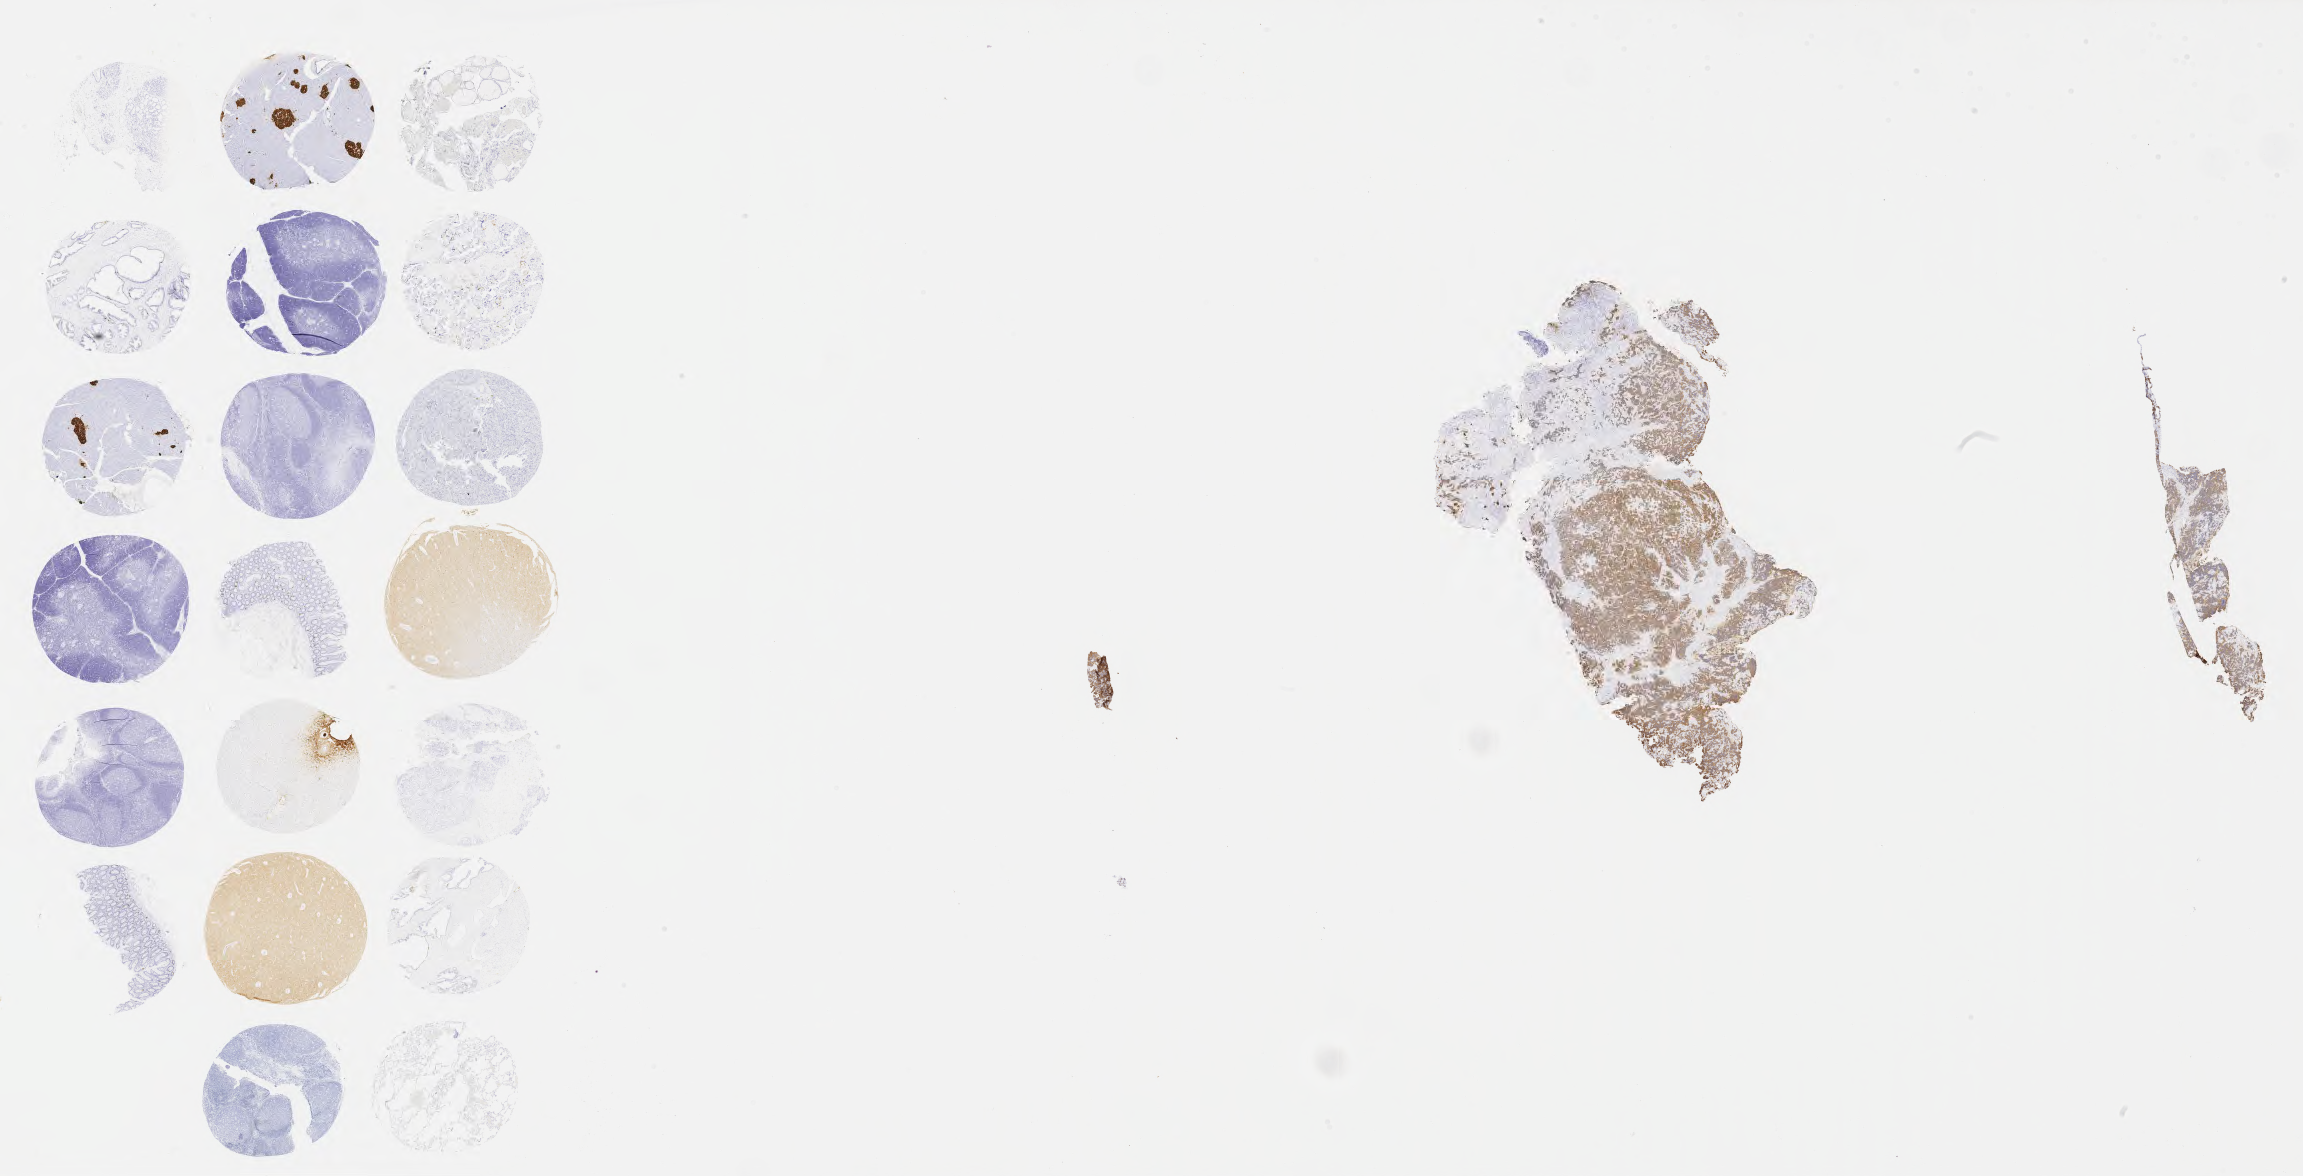
Whole-slide image, immunohistochemical stain for chromogranin, a low-resolution overview of the entire scanned area, about 37.2 x 19.0 mm. Specimen: tumor tissue. Anatomic site: cervix. Patient: female, age 43 years.
- histologic diagnosis: Lymphoepithelial carcinoma